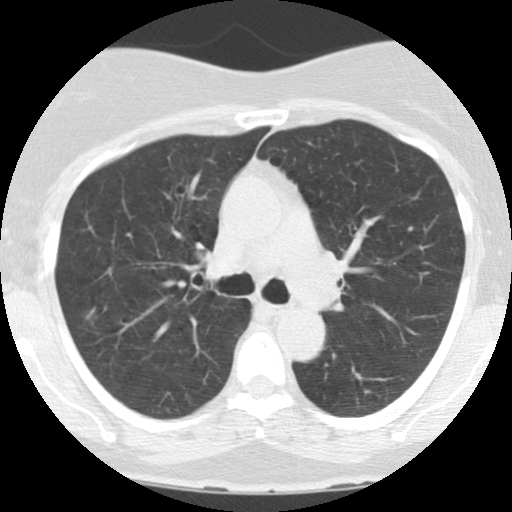
Low-dose screening chest CT, axial slice. Baseline screening round. Lung window (W 1500 / L -600 HU). 2.5 mm slice thickness. 120 kVp. 512 × 512 image matrix. Female participant, aged 60 years at enrolment. Former smoker at enrolment.
Expert-annotated lung lesion, bounding box (x1, y1, x2, y2) in pixels: (69, 297, 109, 335). The screening reader recorded 3 non-calcified nodules or masses ≥4 mm on this exam (left upper lobe, right upper lobe, right upper lobe); which of them this box marks is not recorded. Later outcome: lung cancer diagnosed 31 days after this screen — bronchiolo-alveolar adenocarcinoma, NOS, left upper lobe, moderately differentiated (G2), stage IA (AJCC 6th edition), 15 mm at pathology.